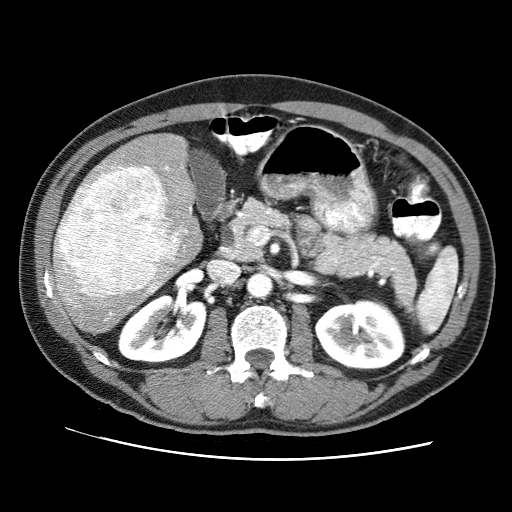
Contrast-enhanced abdominal CT (liver protocol), one axial slice; position 36 of 71 along the scan axis; reconstruction kernel STANDARD; soft-tissue window (W 400 / L 40 HU); 2.5 mm slice thickness; 512 × 512 image matrix, field of view 360 × 360 mm. Case-level facts recorded for this patient, not image findings: diagnosis: hepatocellular carcinoma (patient treated with transarterial chemoembolisation; whether this scan precedes or follows treatment is not stated here); TNM stage (as recorded): Stage-II; Child-Pugh class: A; tumour nodularity: multinodular; tumour size: 4.6 cm.
Outlined on this slice (semi-automatically segmented with operator editing):
- liver parenchyma outside the tumour (the mass and vessels are separate outlines, so this box may not span the whole liver): bounding box (x1, y1, x2, y2) in pixels: (54, 132, 203, 333)
- mass: (57, 166, 179, 297)
- liver vessels: (57, 166, 192, 315)